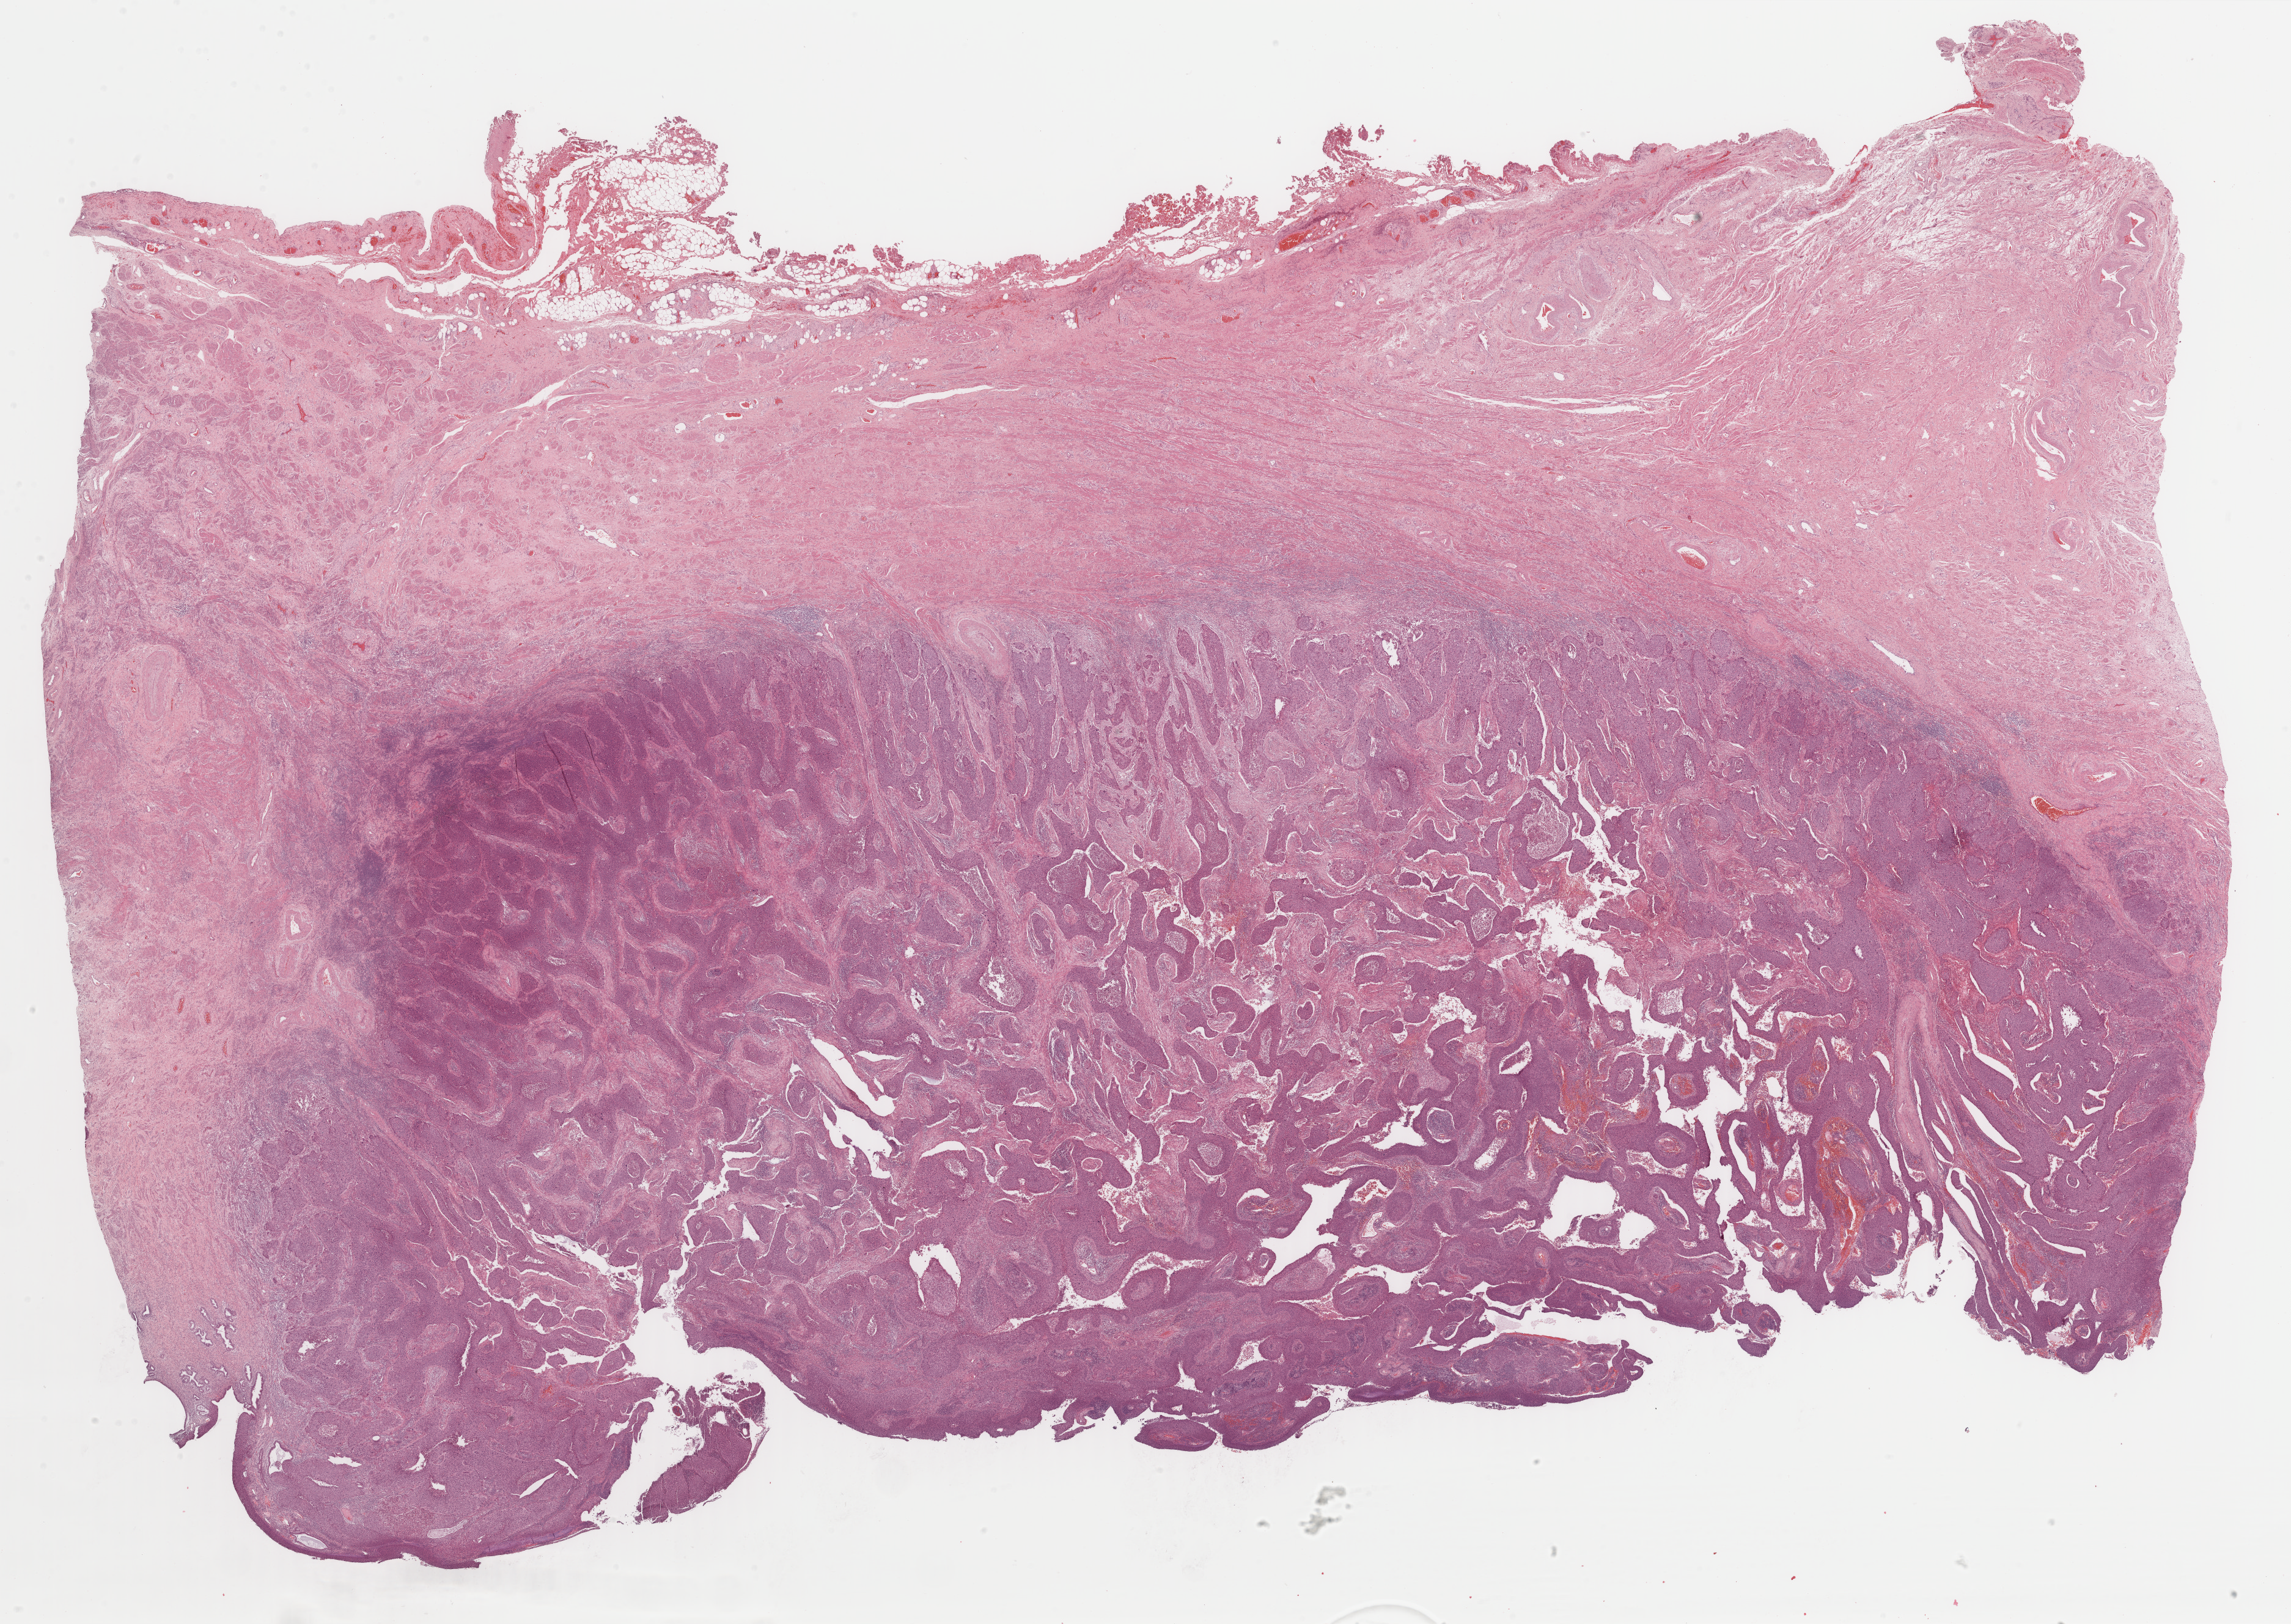
H&E-stained whole-slide image, low-resolution overview of the scanned area, about 29.7 x 21.1 mm (from a 40x scan), formalin-fixed paraffin-embedded (FFPE) diagnostic section, sample: primary tumour, cervix. Female, age 53 years at initial diagnosis.
Pathologic diagnosis: Squamous cell carcinoma, NOS (cervix uteri).